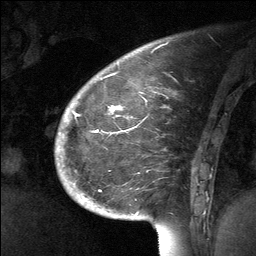
Breast MRI (dynamic contrast-enhanced), one sagittal slice. Position 18 of 64 along the scan axis. Dynamic contrast-enhanced study with each time point stored as its own series, time point 2 of 3 at this slice position (early post-contrast, ordered by acquisition time). 1.5 T. TE 4.8 ms, TR 27 ms. 2 mm slice thickness. 256 × 256 image matrix, field of view 200 × 200 mm. Female patient, age 39 years. Case-level facts recorded for this patient, not image findings: setting: breast cancer imaged before/during neoadjuvant chemotherapy; receptor status: HER2-positive.
Structures marked on this image (semi-automatically segmented with operator editing):
- analysis volume of interest (the breast-tissue region the enhancement analysis was run in; not a lesion): box from (x=70, y=69) to (x=202, y=224) px
- tumour enhancement mask (voxels above the 90 % enhancement threshold inside the analysis volume of interest): (x=77, y=105)–(x=122, y=132)